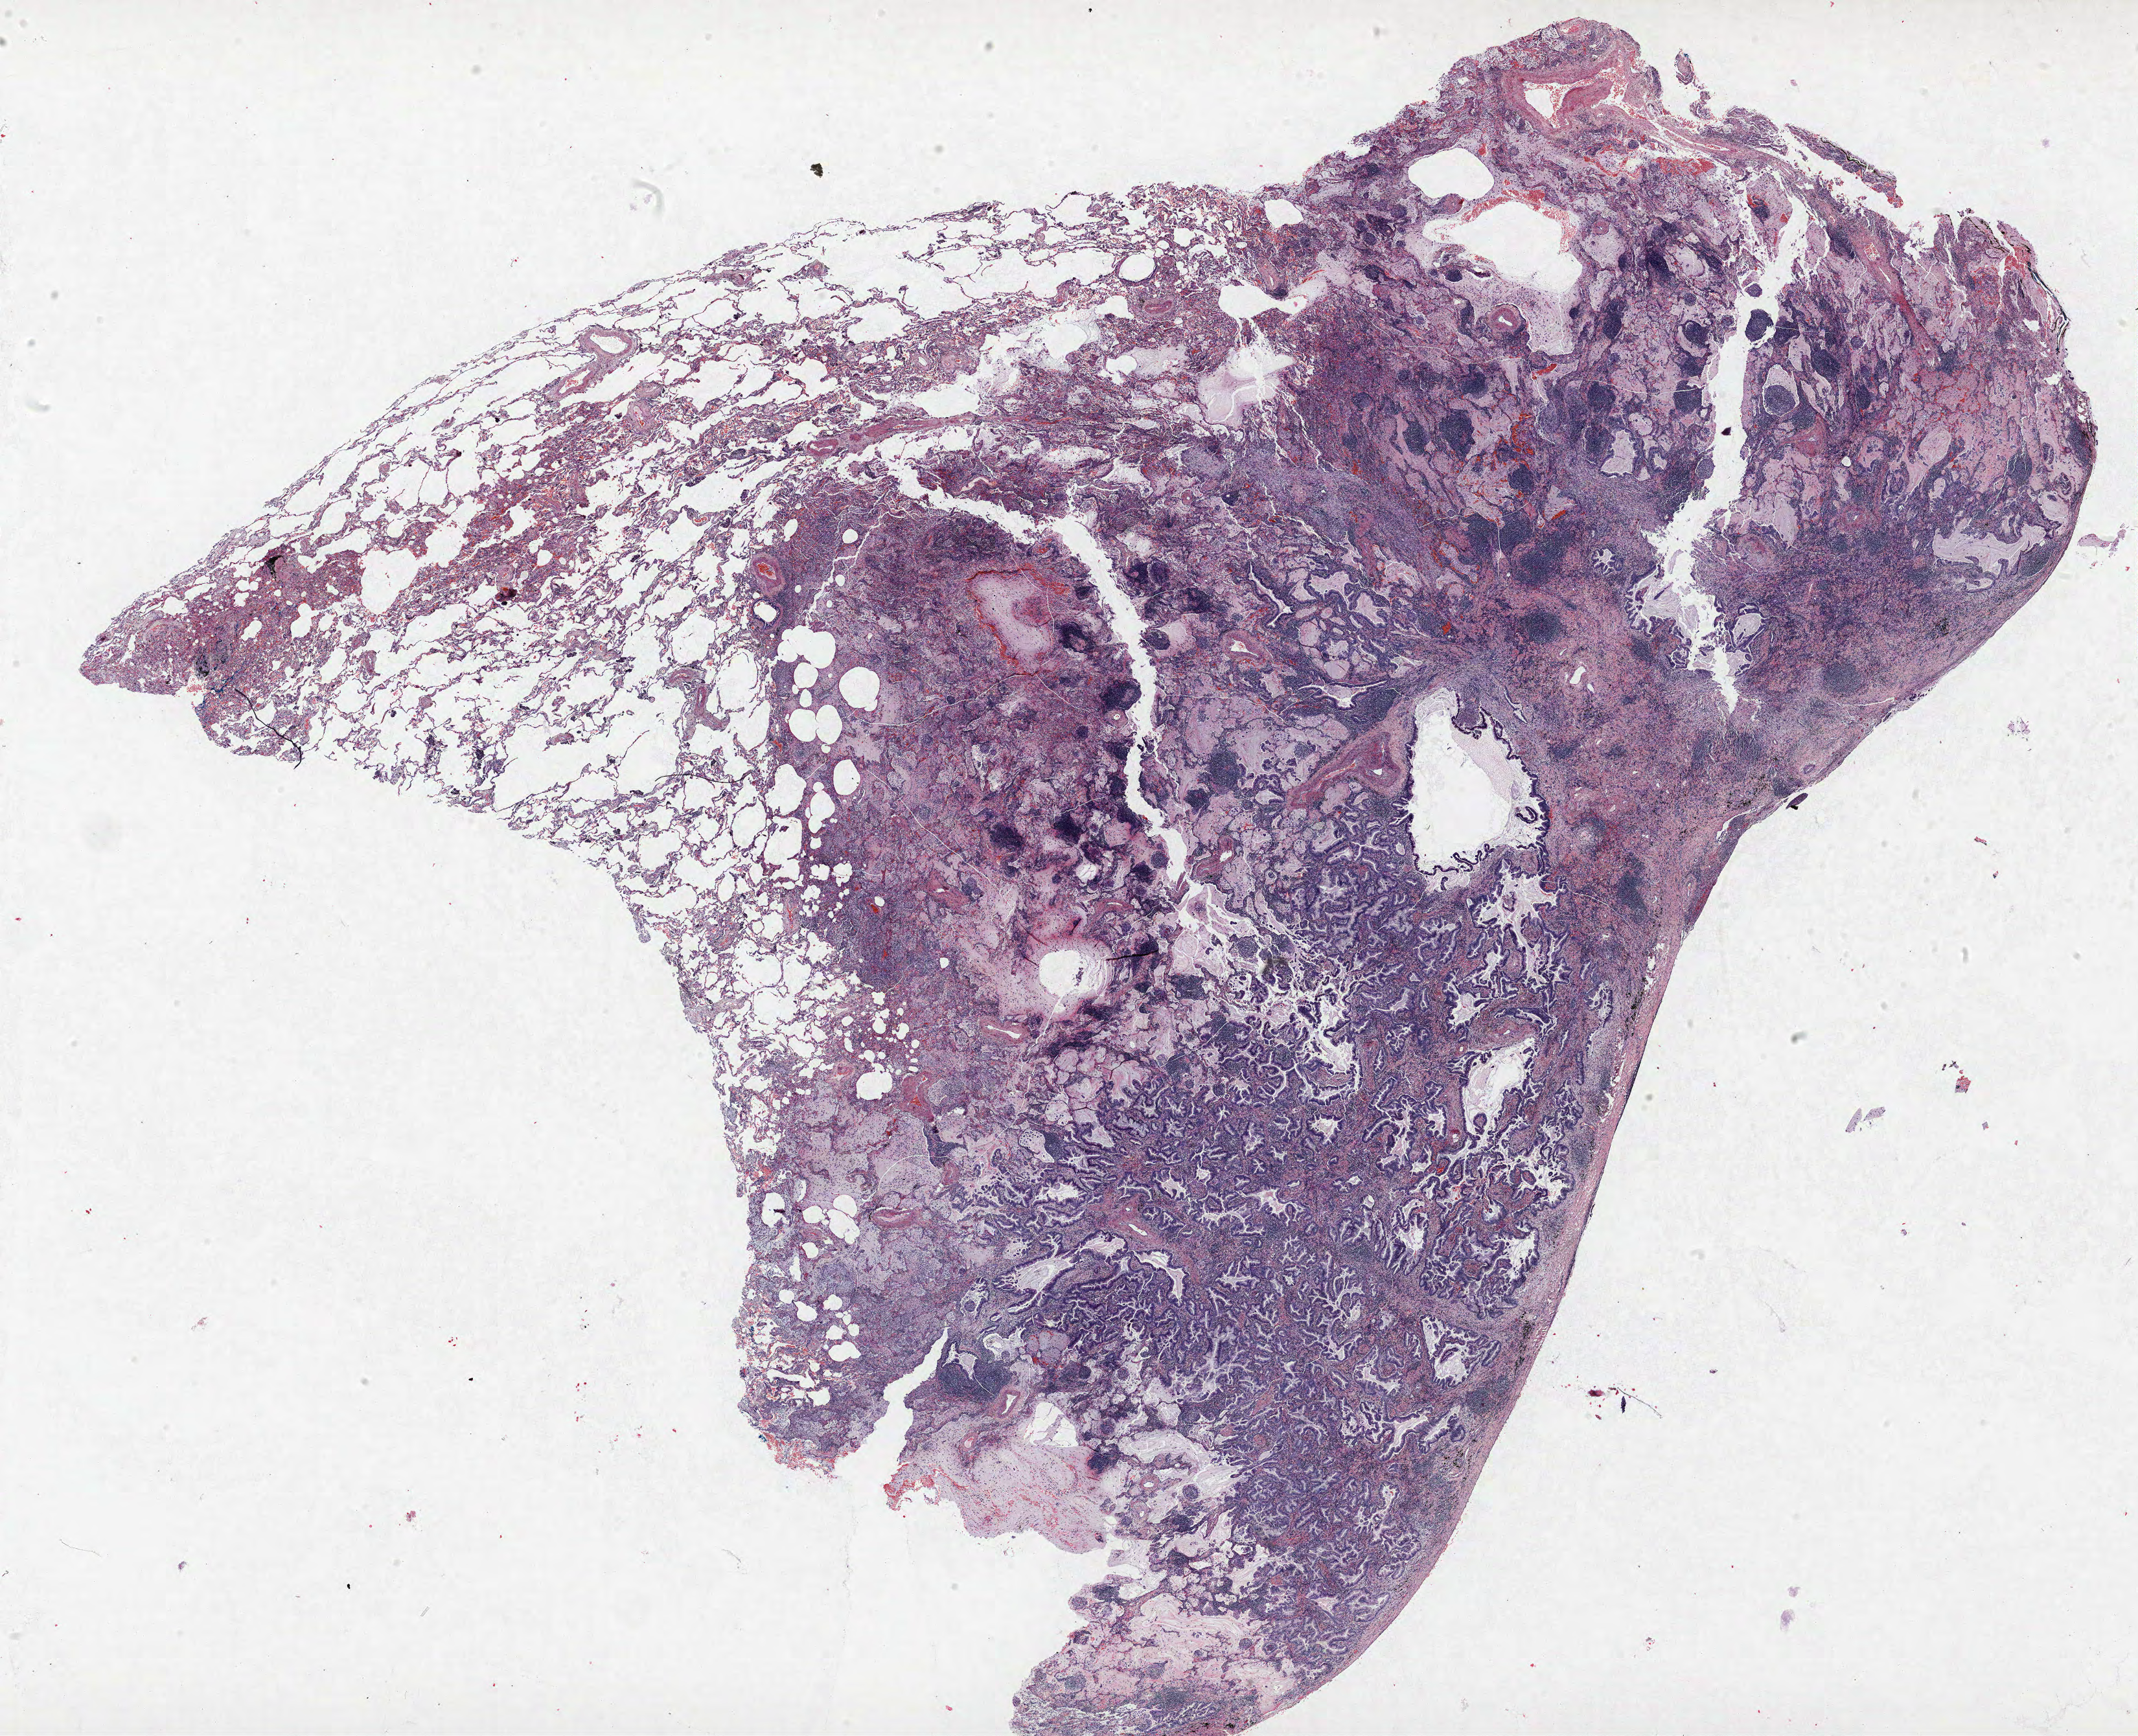
Whole-slide histology image, H&E, low-resolution overview of the scanned area, about 26.4 x 21.4 mm, FFPE section, lung tissue. Male patient, aged 73 at enrolment. Former smoker at enrolment.
Participant's lung-cancer diagnosis: Adenocarcinoma, NOS (ICD-O-3 8140/3).